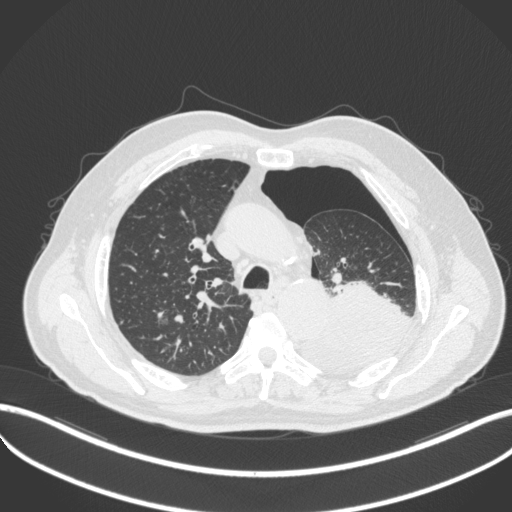
Chest CT, one axial slice; position 361 of 466 along the scan axis; reconstruction kernel B31f; 120 kVp; lung window (W 1500 / L -600 HU); 1 mm slice thickness; 512 × 512 image matrix, field of view 400 × 400 mm. Male patient, age 76 years. From the clinical record (not read from this slice): clinical TNM (as recorded): T3 N0 M1b.
Structures marked on this image (rectangle marked by the reading radiologist):
- lung tumour (recorded histology: adenocarcinoma): bounding box (x1, y1, x2, y2) in pixels: (298, 276, 416, 375)